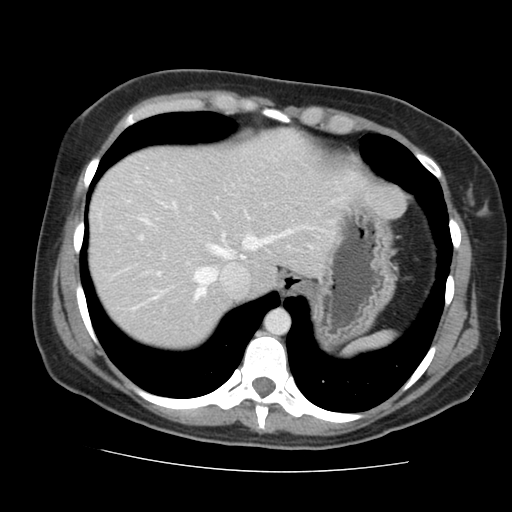
Contrast-enhanced abdominal CT, one axial slice; position 125 of 144 along the scan axis; 120 kVp; soft-tissue window (W 400 / L 40 HU); 2.5 mm slice thickness; 512 × 512 image matrix. Female patient, age 46 years. Case-level facts recorded for this patient, not image findings: diagnosis: colorectal cancer liver metastases, imaged before liver resection; multiple liver metastases: no; largest metastasis: 2.8 cm.
Annotated regions visible in this slice (outlined manually by an expert reader):
- hepatic veins: bounding box (x1, y1, x2, y2) in pixels: (142, 196, 345, 300)
- liver: (90, 131, 343, 349)
- planned liver remnant (the part of the liver to remain after resection): (90, 131, 343, 349)
- portal vein (with intrahepatic branches): (140, 238, 159, 275)